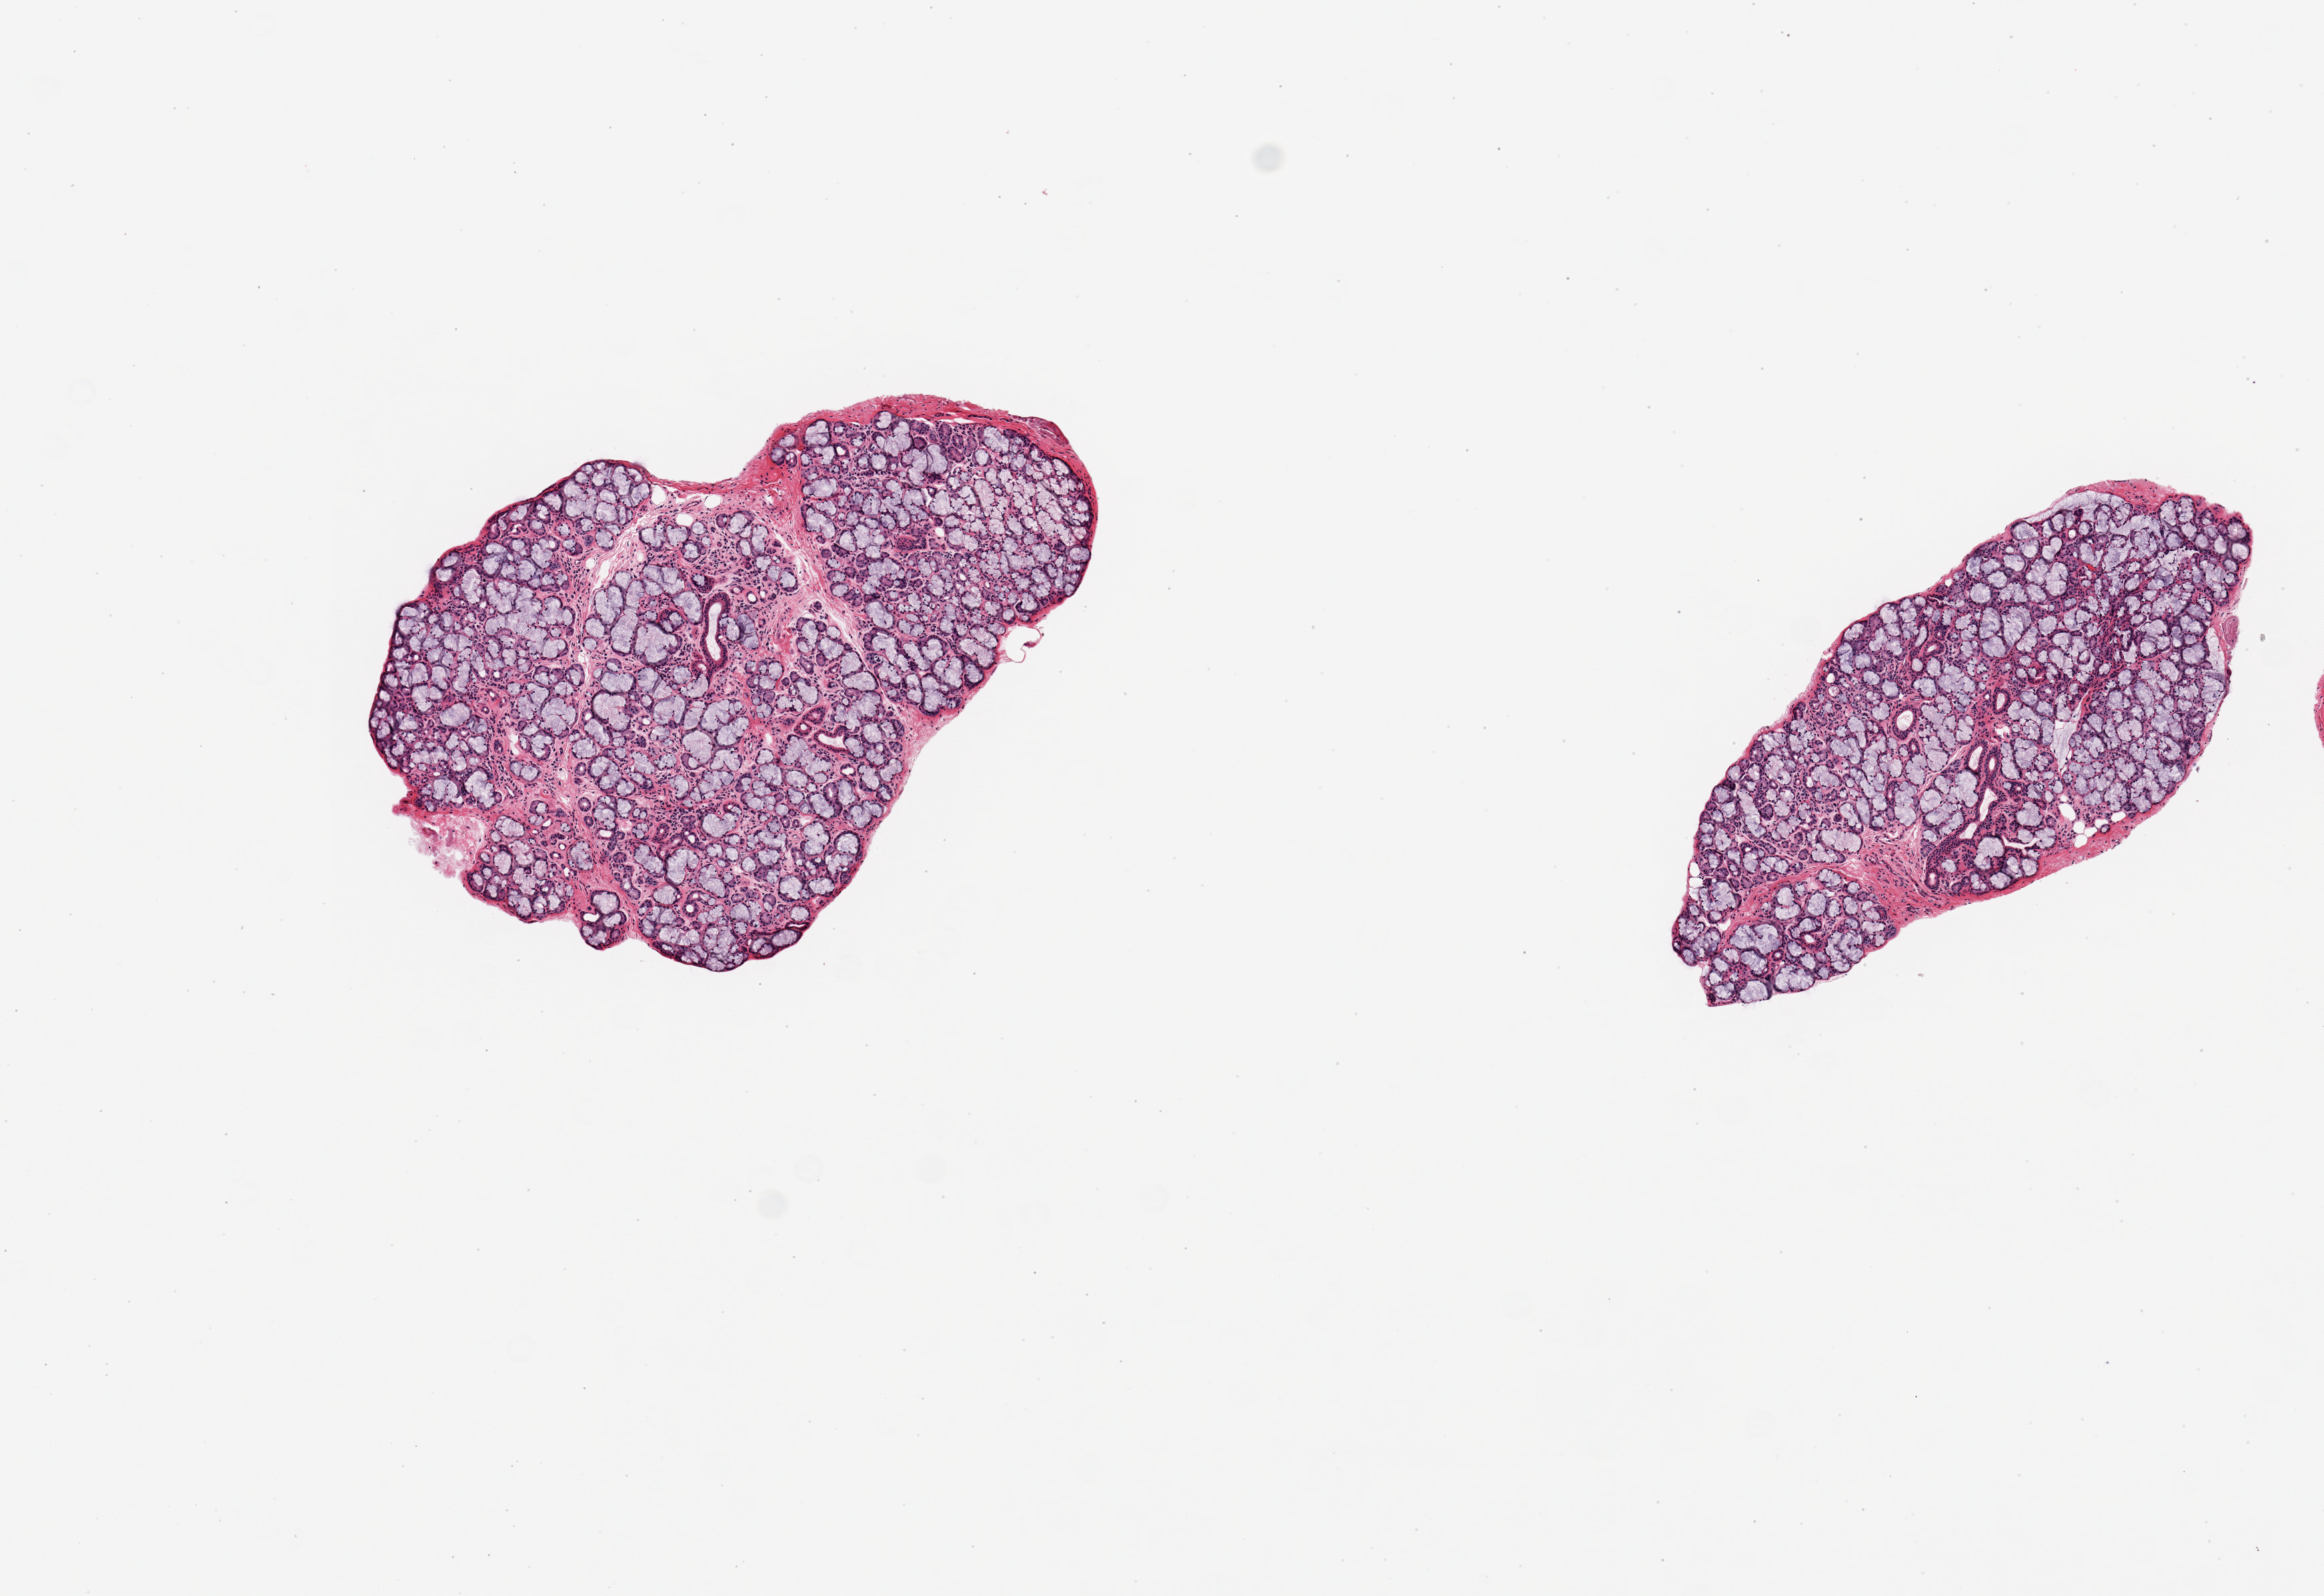
Whole-slide image, haematoxylin and eosin stain, brightfield, shown as a low-resolution overview of the whole scanned area (about 6.9 x 4.7 mm, slide scanned at 20x); PAXgene-fixed paraffin-embedded (PFPE) section; sampled site (target tissue): minor salivary gland; tissue donor sample. Donor sex: female.
Review note (as recorded): 2 pieces, 100% glandular elements, valuable specimen.